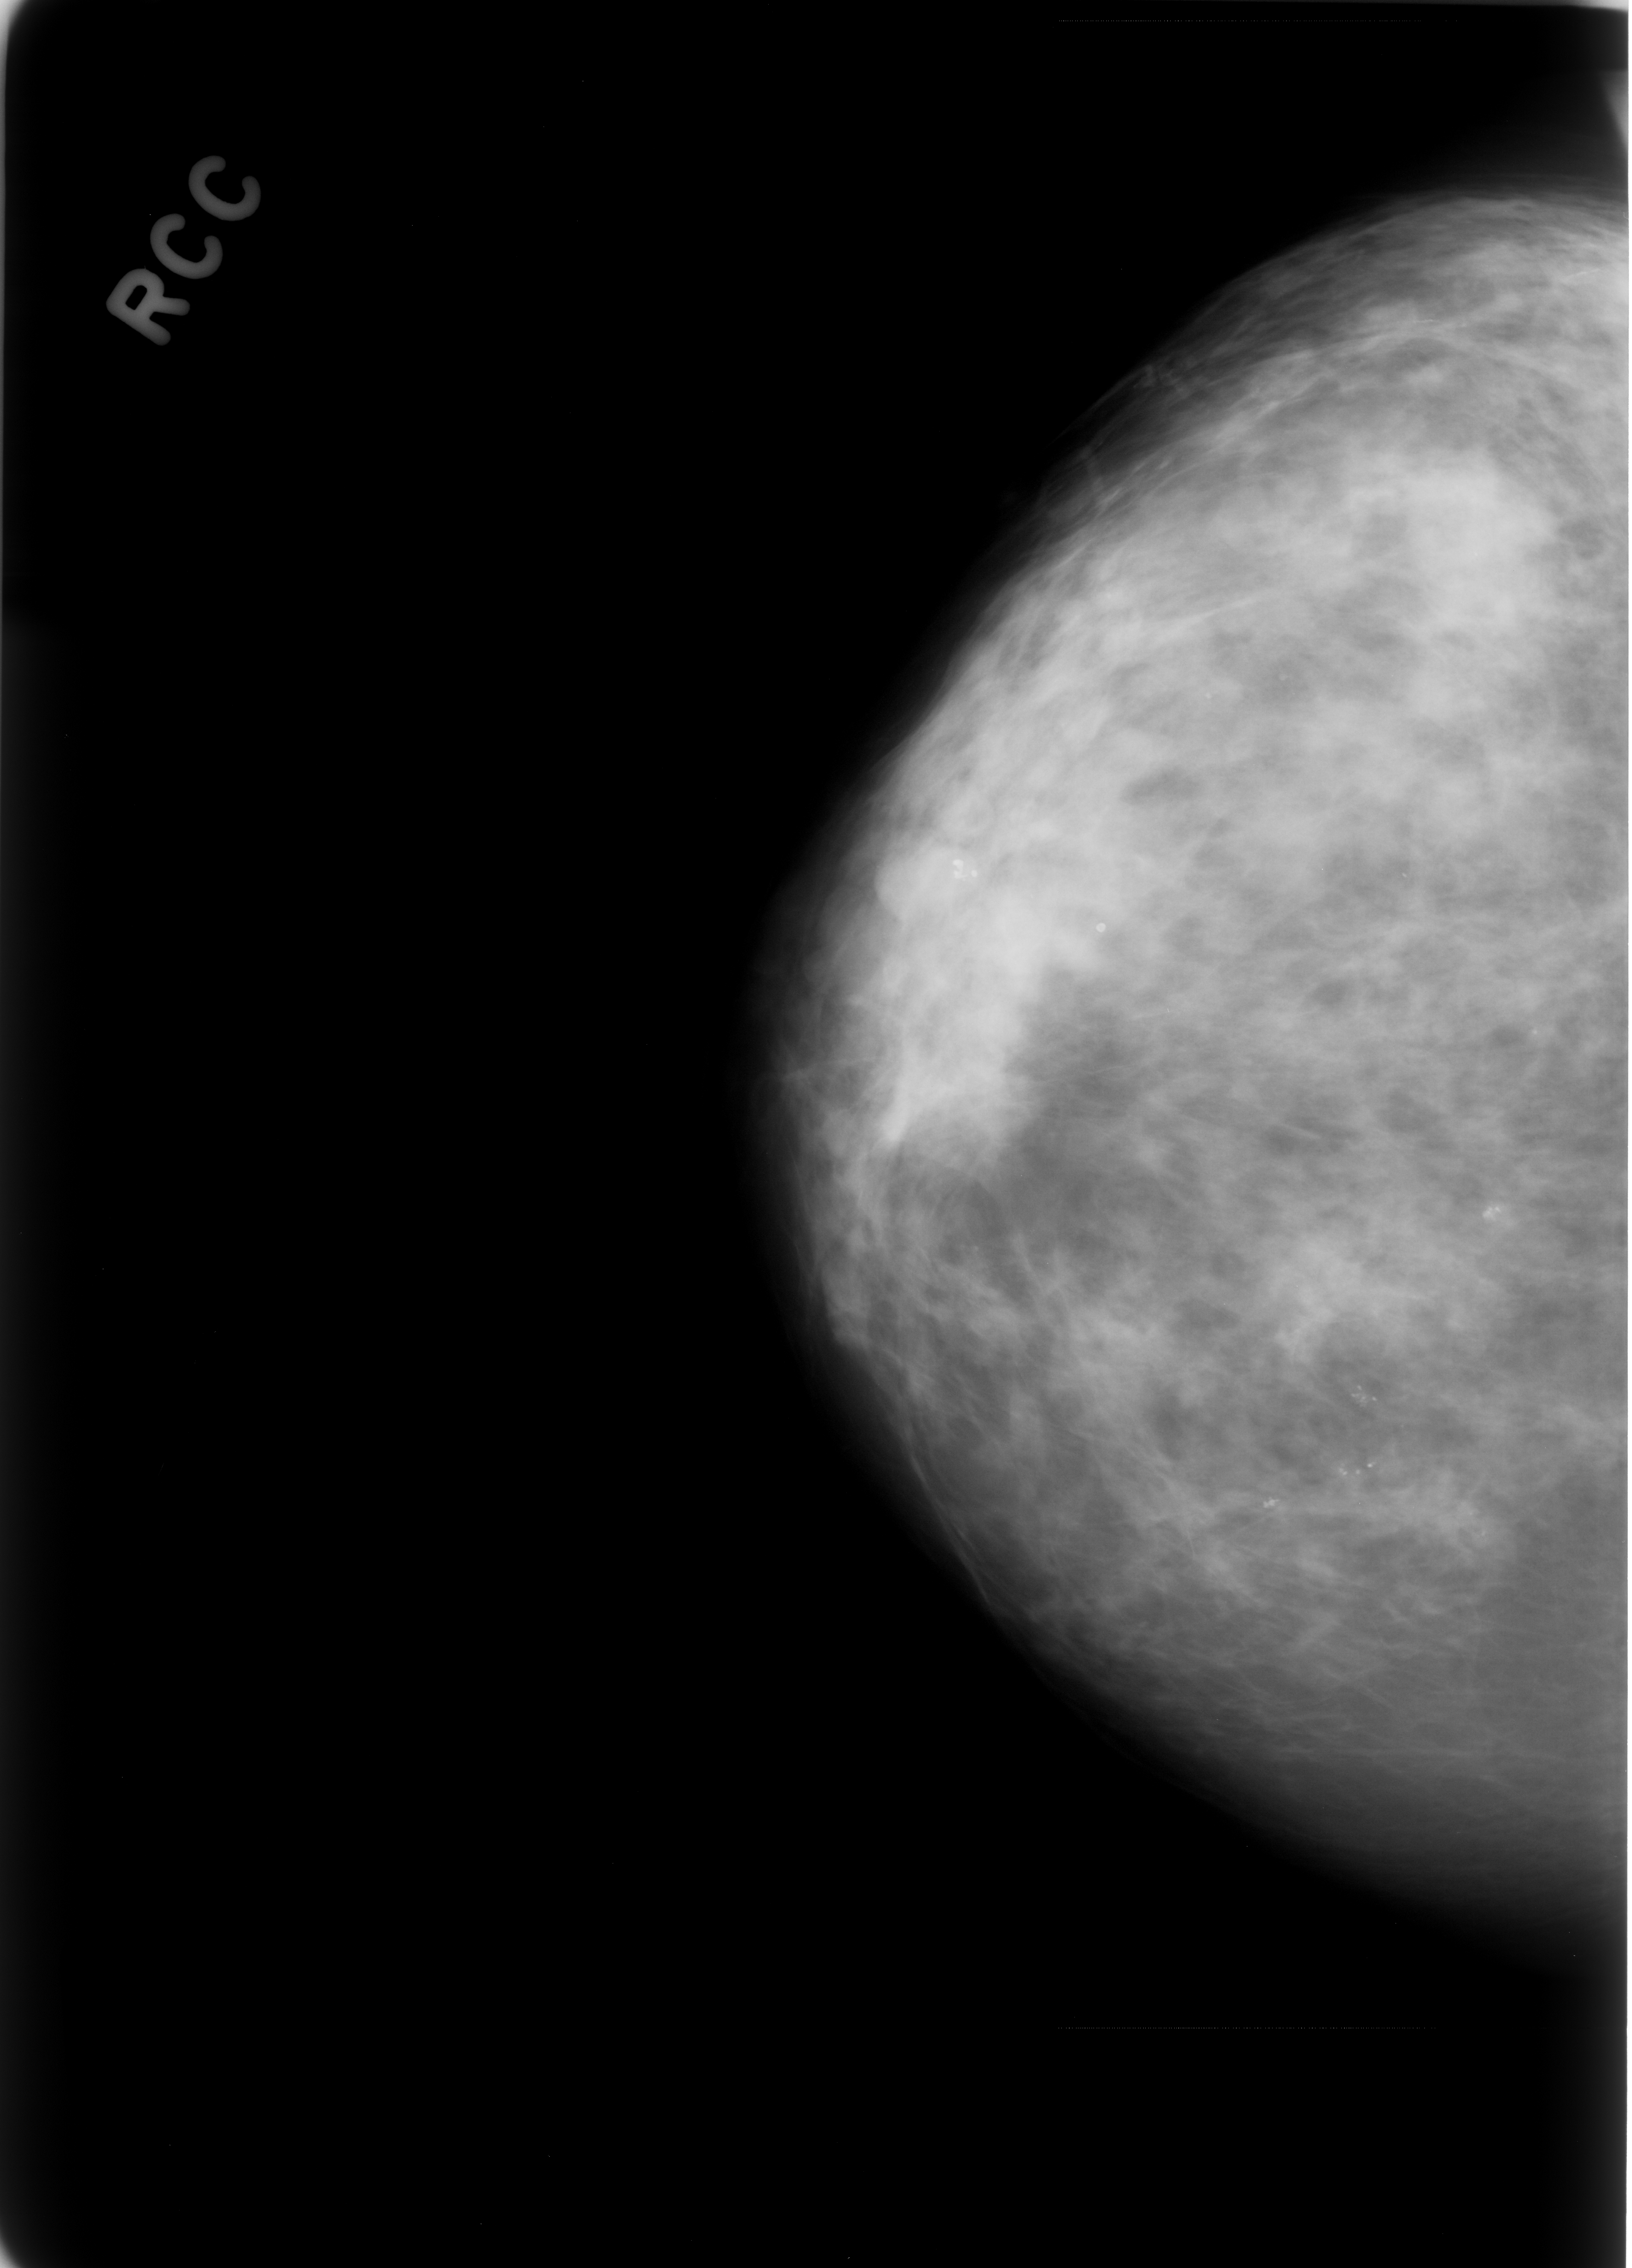
Mammogram (digitized film), right breast, CC view, BI-RADS breast density category 3 (scale 1–4).
Radiologist-marked abnormalities on this image: Finding 1 of 2: calcifications, morphology pleomorphic, distribution clustered; BI-RADS assessment category 4; subtlety rating 4 on a 1 (subtle) to 5 (obvious) scale; pathology result (as recorded, not read from the image): benign. Finding 2 of 2: calcifications, morphology pleomorphic, distribution clustered; BI-RADS assessment category 4; subtlety rating 5 on a 1 (subtle) to 5 (obvious) scale; pathology (as recorded): benign.